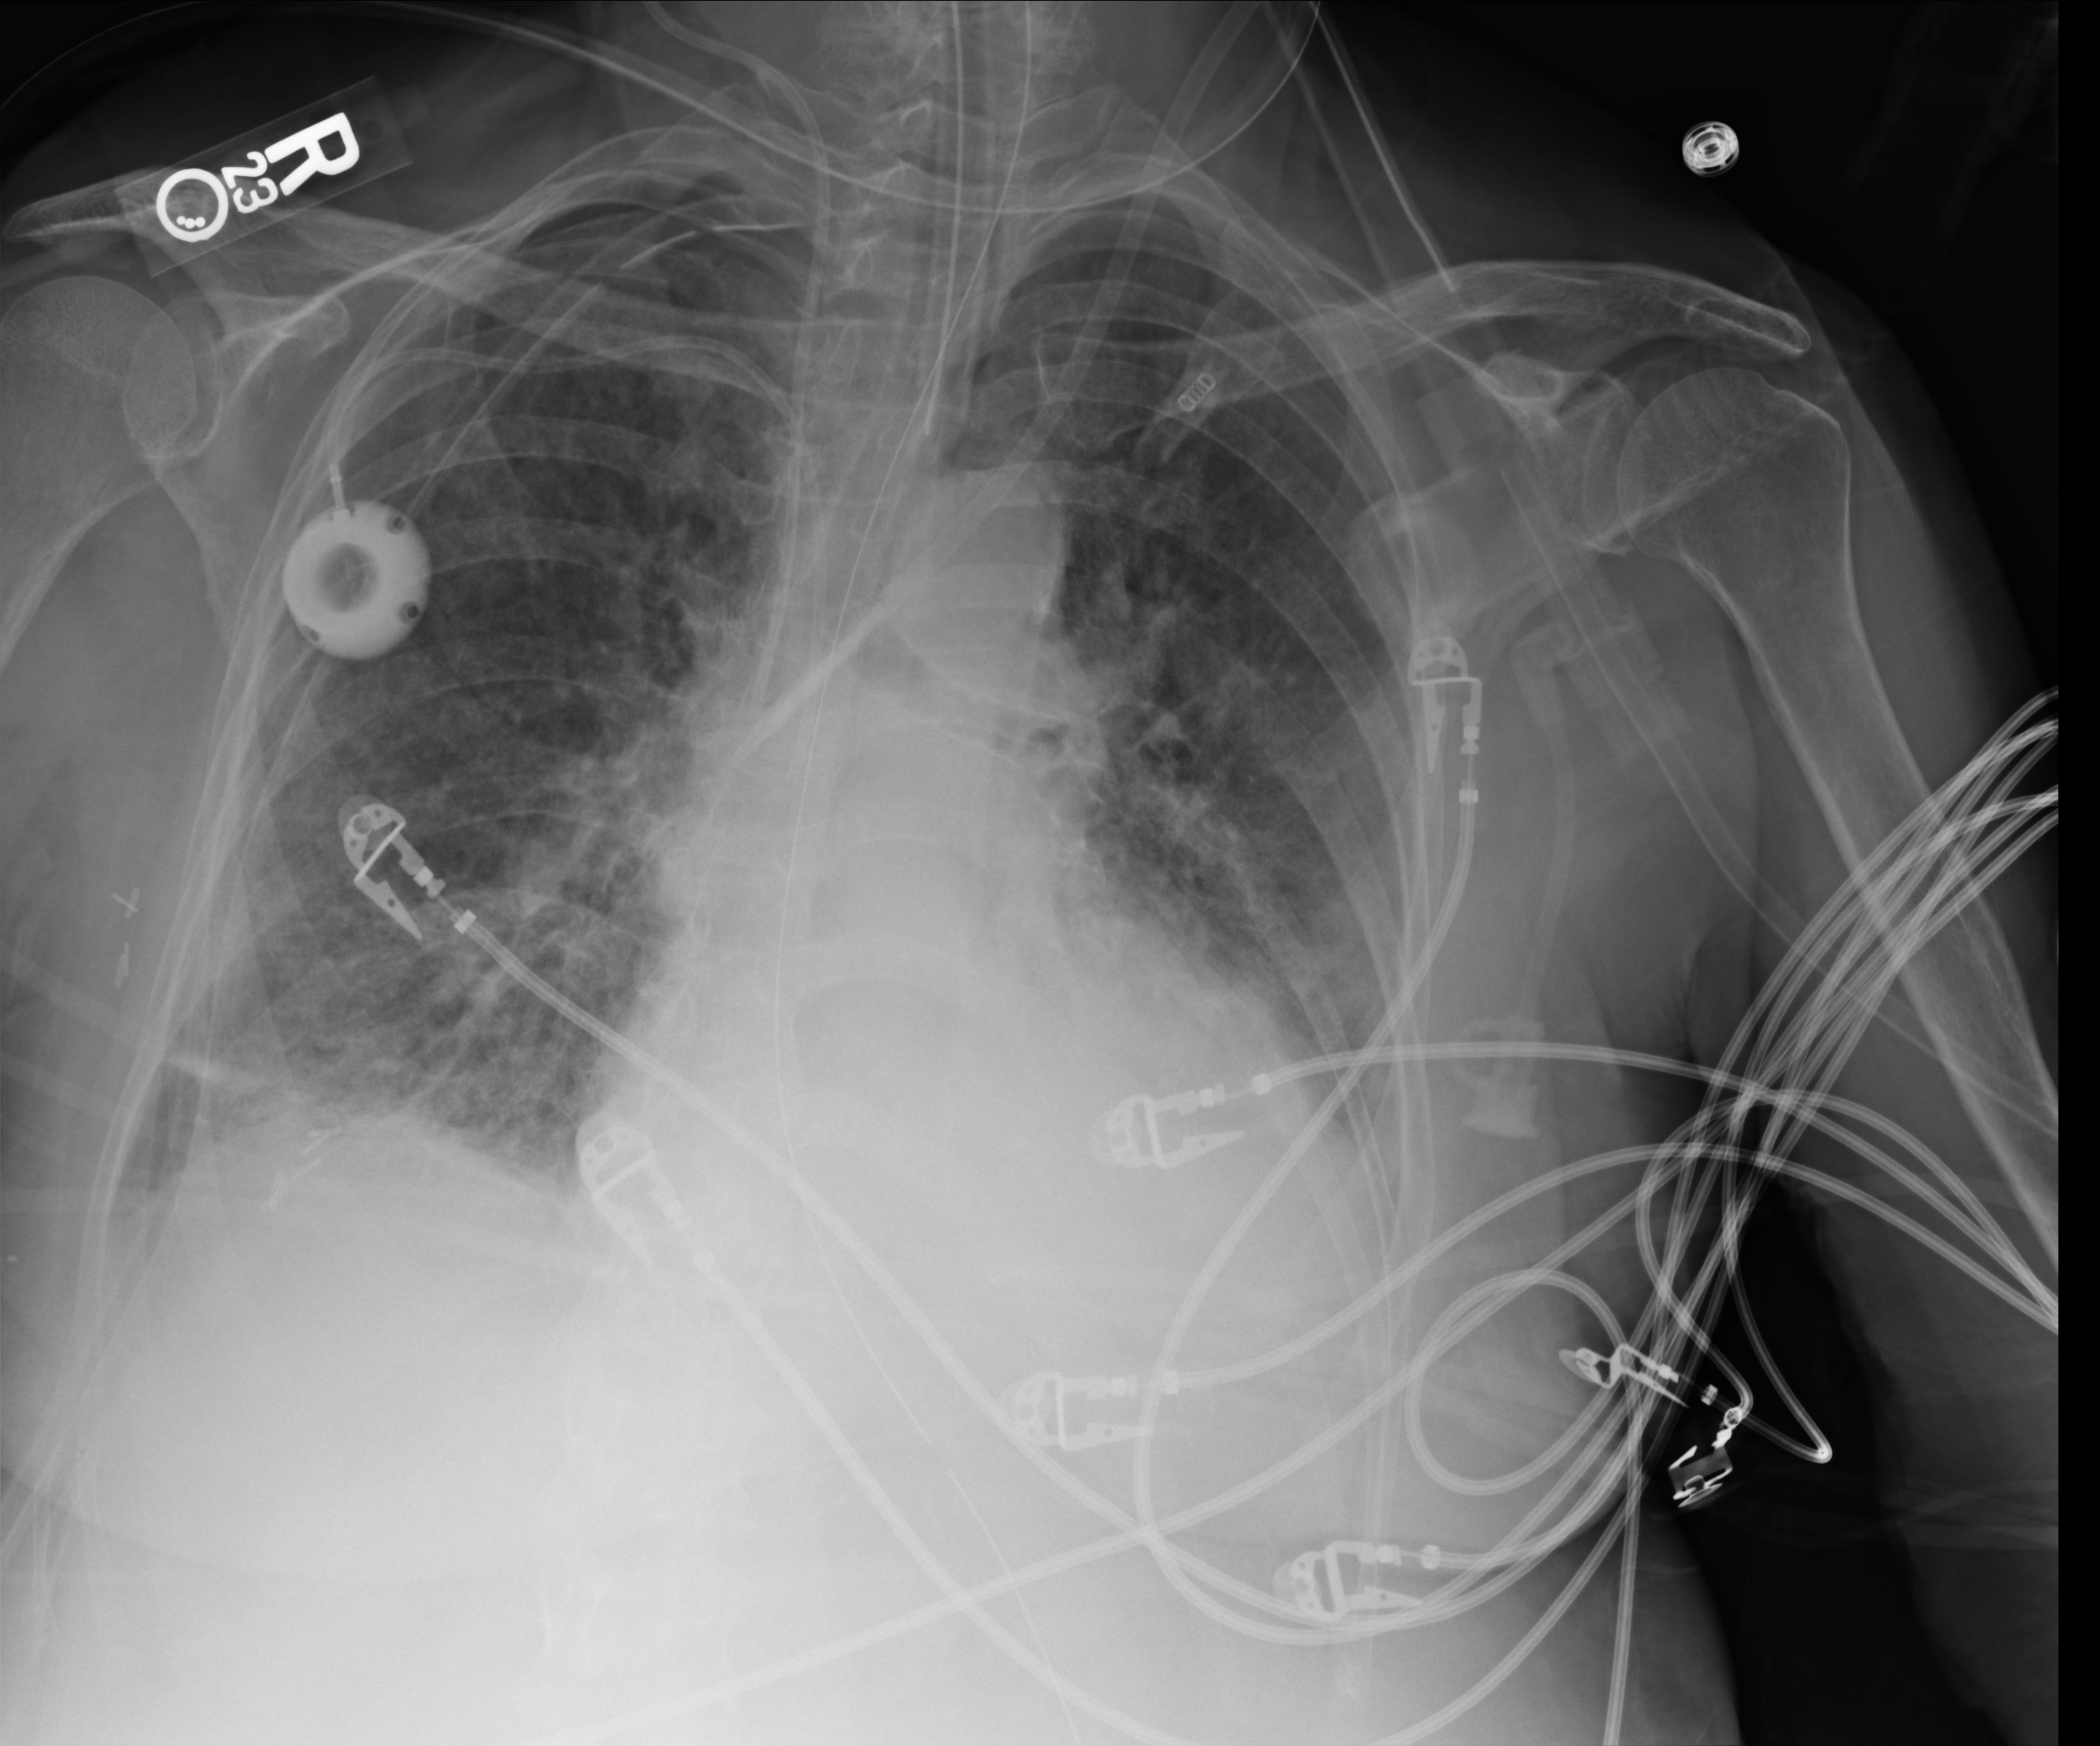
Bedside chest radiograph (computed radiography); anteroposterior (AP) projection. Female patient hospitalised with COVID-19, age 60–74 years.
Admission-level facts for this patient (not findings on this image; timing relative to this image not recorded): mechanically ventilated during this hospital stay: yes; COPD (admission record): no; admitted to intensive care during this hospital stay: yes.